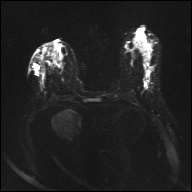
Breast MRI, one axial slice. Position 15 of 32 along the scan axis. Diffusion-weighted series; image 2 of 4 stored at this slice position (different b-values; order by instance number). 1.5 T. 192 × 192 image matrix, field of view 360 × 360 mm. Female patient.
Annotated regions visible in this slice (manually delineated by an expert):
- tumour on diffusion-weighted imaging: bounding box (x1, y1, x2, y2) in pixels: (145, 79, 149, 82)